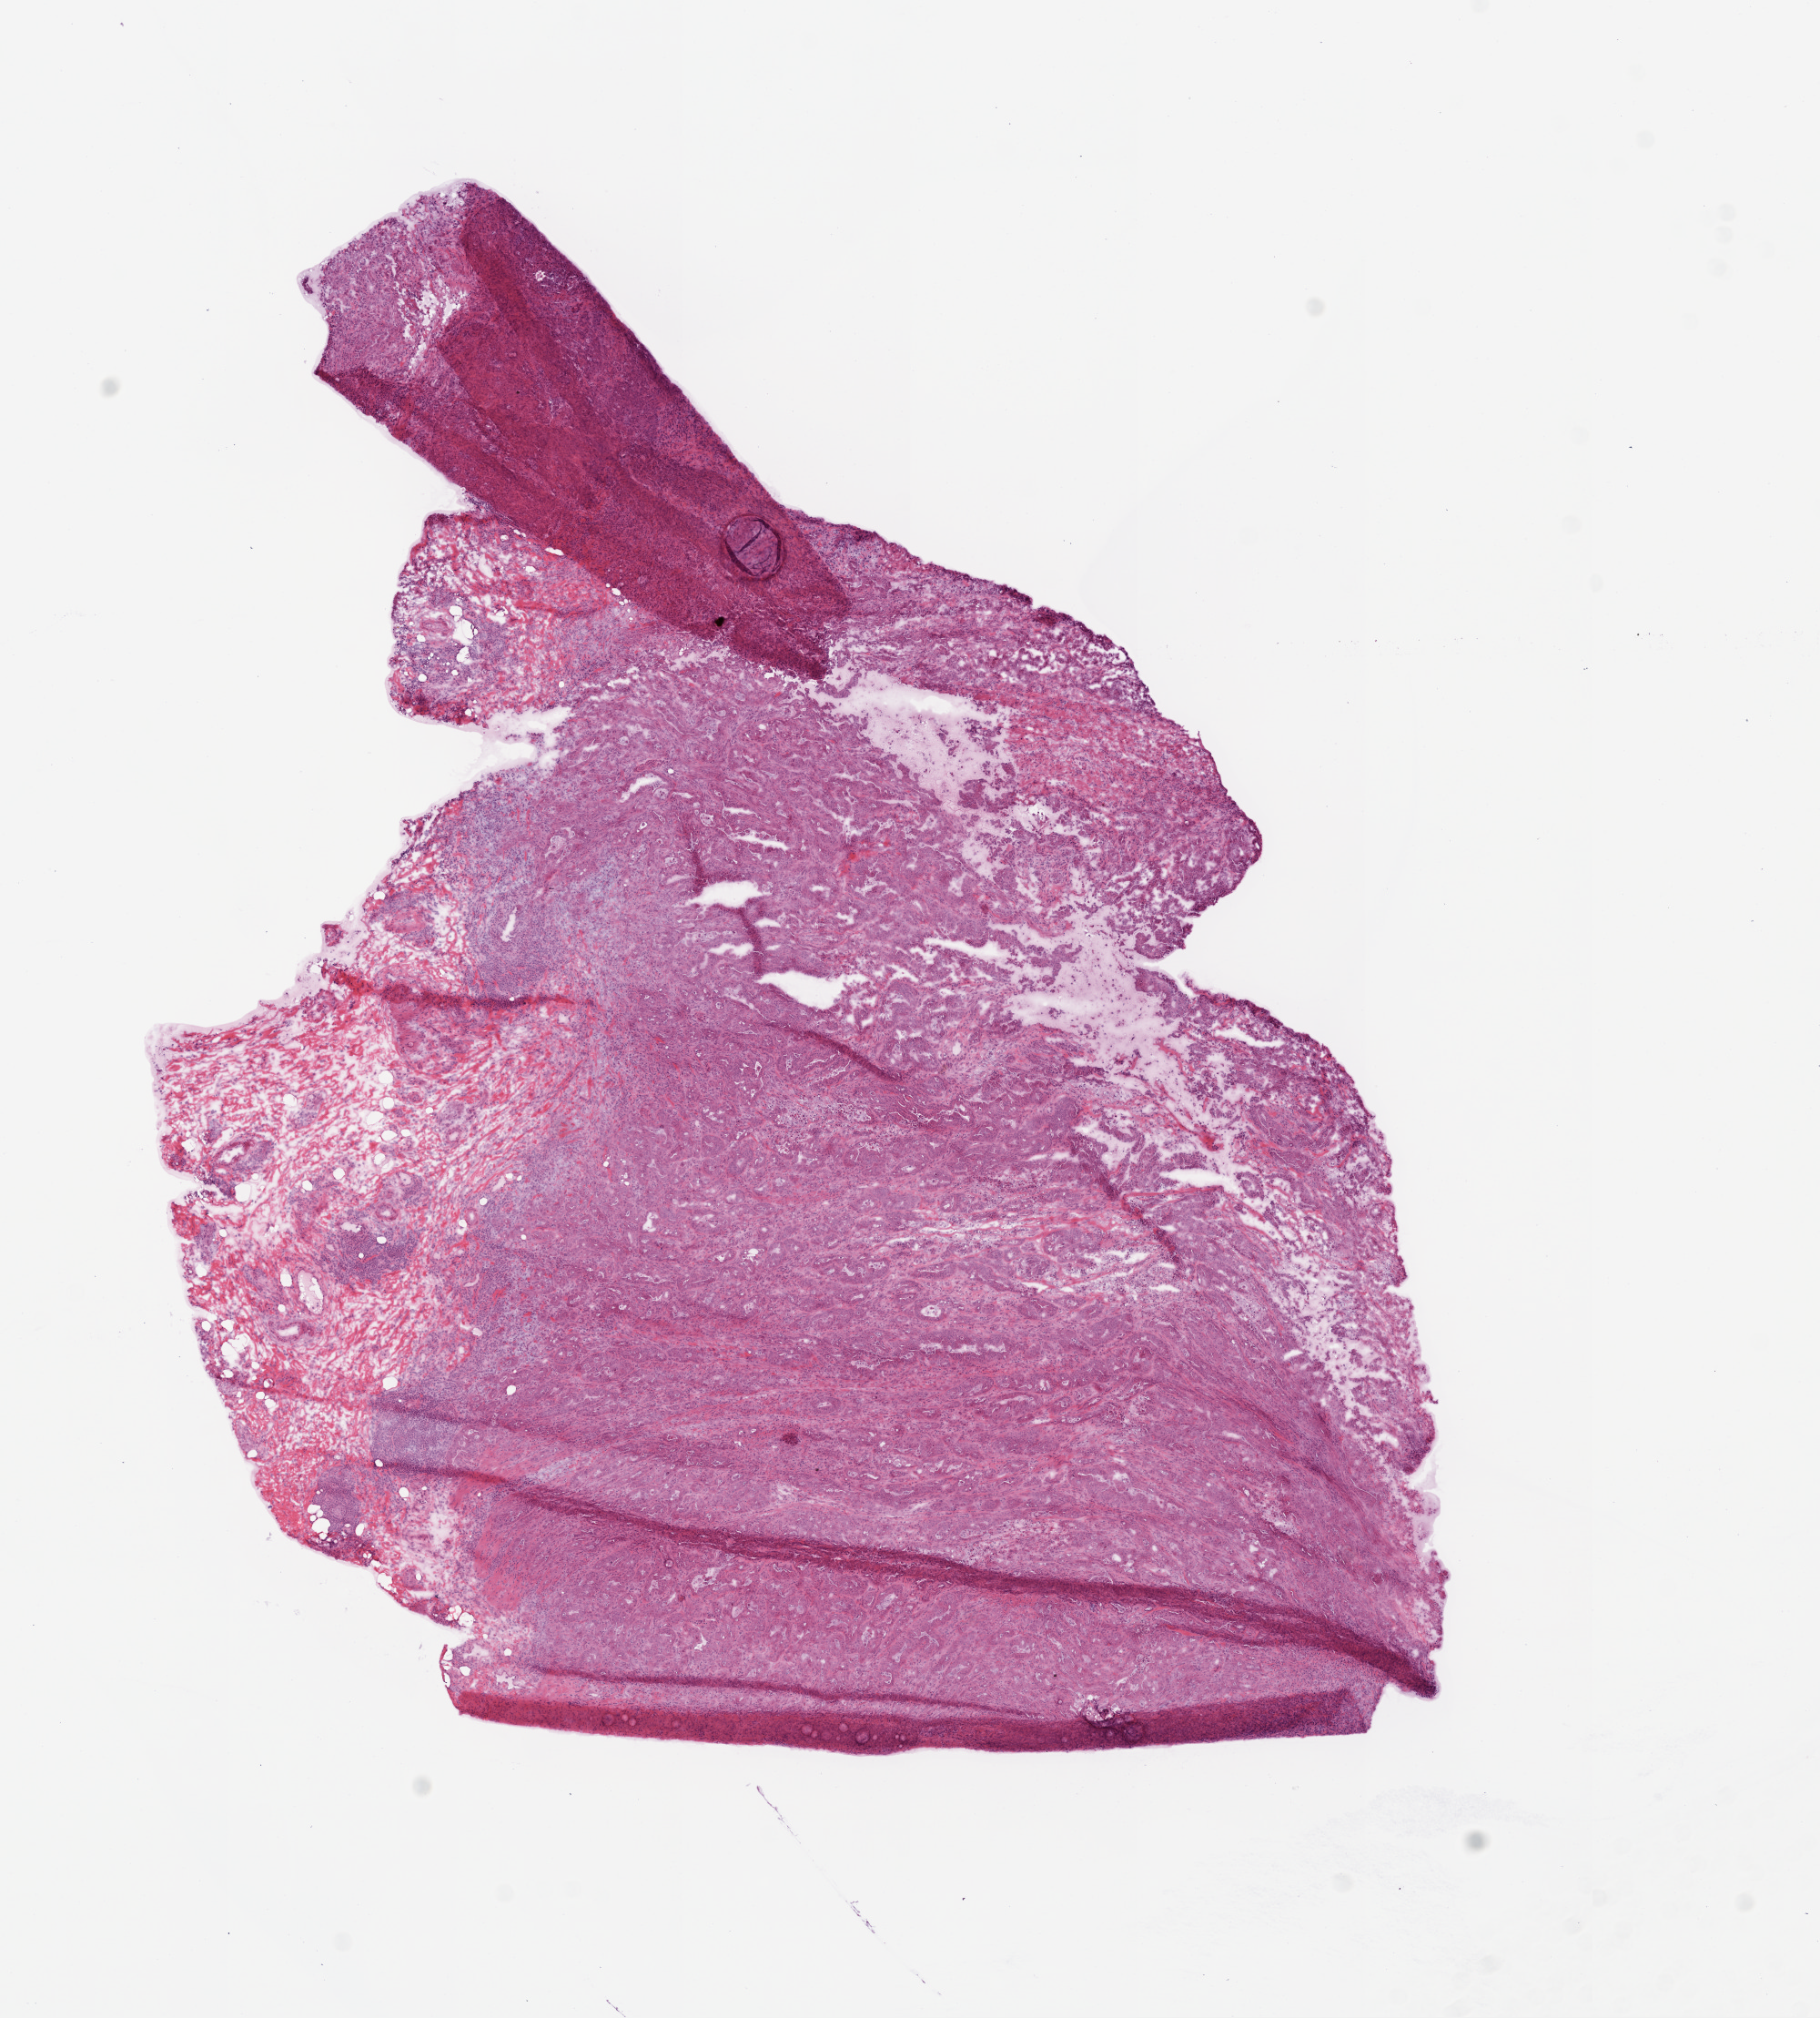
H&E whole-slide image, whole scanned area (about 8.0 x 8.9 mm) shown as a low-resolution overview; frozen section from the top of the tissue portion; primary tumour sample from the colon. Female patient; age at initial diagnosis 71 years. Pathologist review of this section (percent, as recorded): tumour cells 80%, tumour nuclei 85%, normal cells 10%, stromal cells 5%, necrosis 5%.
* lymph nodes positive (case pathology): 5 of 23 examined
* AJCC pathologic stage: IV (6th edition)
* histologic diagnosis: Adenocarcinoma, NOS (ascending colon)